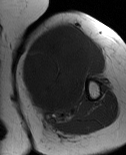
MRI of an extremity soft-tissue mass, one axial slice. Position 49 of 86 along the scan axis. MR volume resampled by the dataset authors to the PET/CT grid (not the native acquisition matrix). 3.27 mm slice thickness. 126 × 155 image matrix. Female patient. Case-level facts recorded for this patient, not image findings: histological type: pleiomorphic leiomyosarcoma; grade: high; site of the primary tumour: left biceps.
Structures marked on this image (expert contour drawn on MRI and transferred to this co-registered scan by the dataset authors):
- gross tumour volume including surrounding oedema: box from (x=20, y=24) to (x=99, y=121) px
- gross tumour volume (mass): (x=22, y=24)–(x=92, y=114)